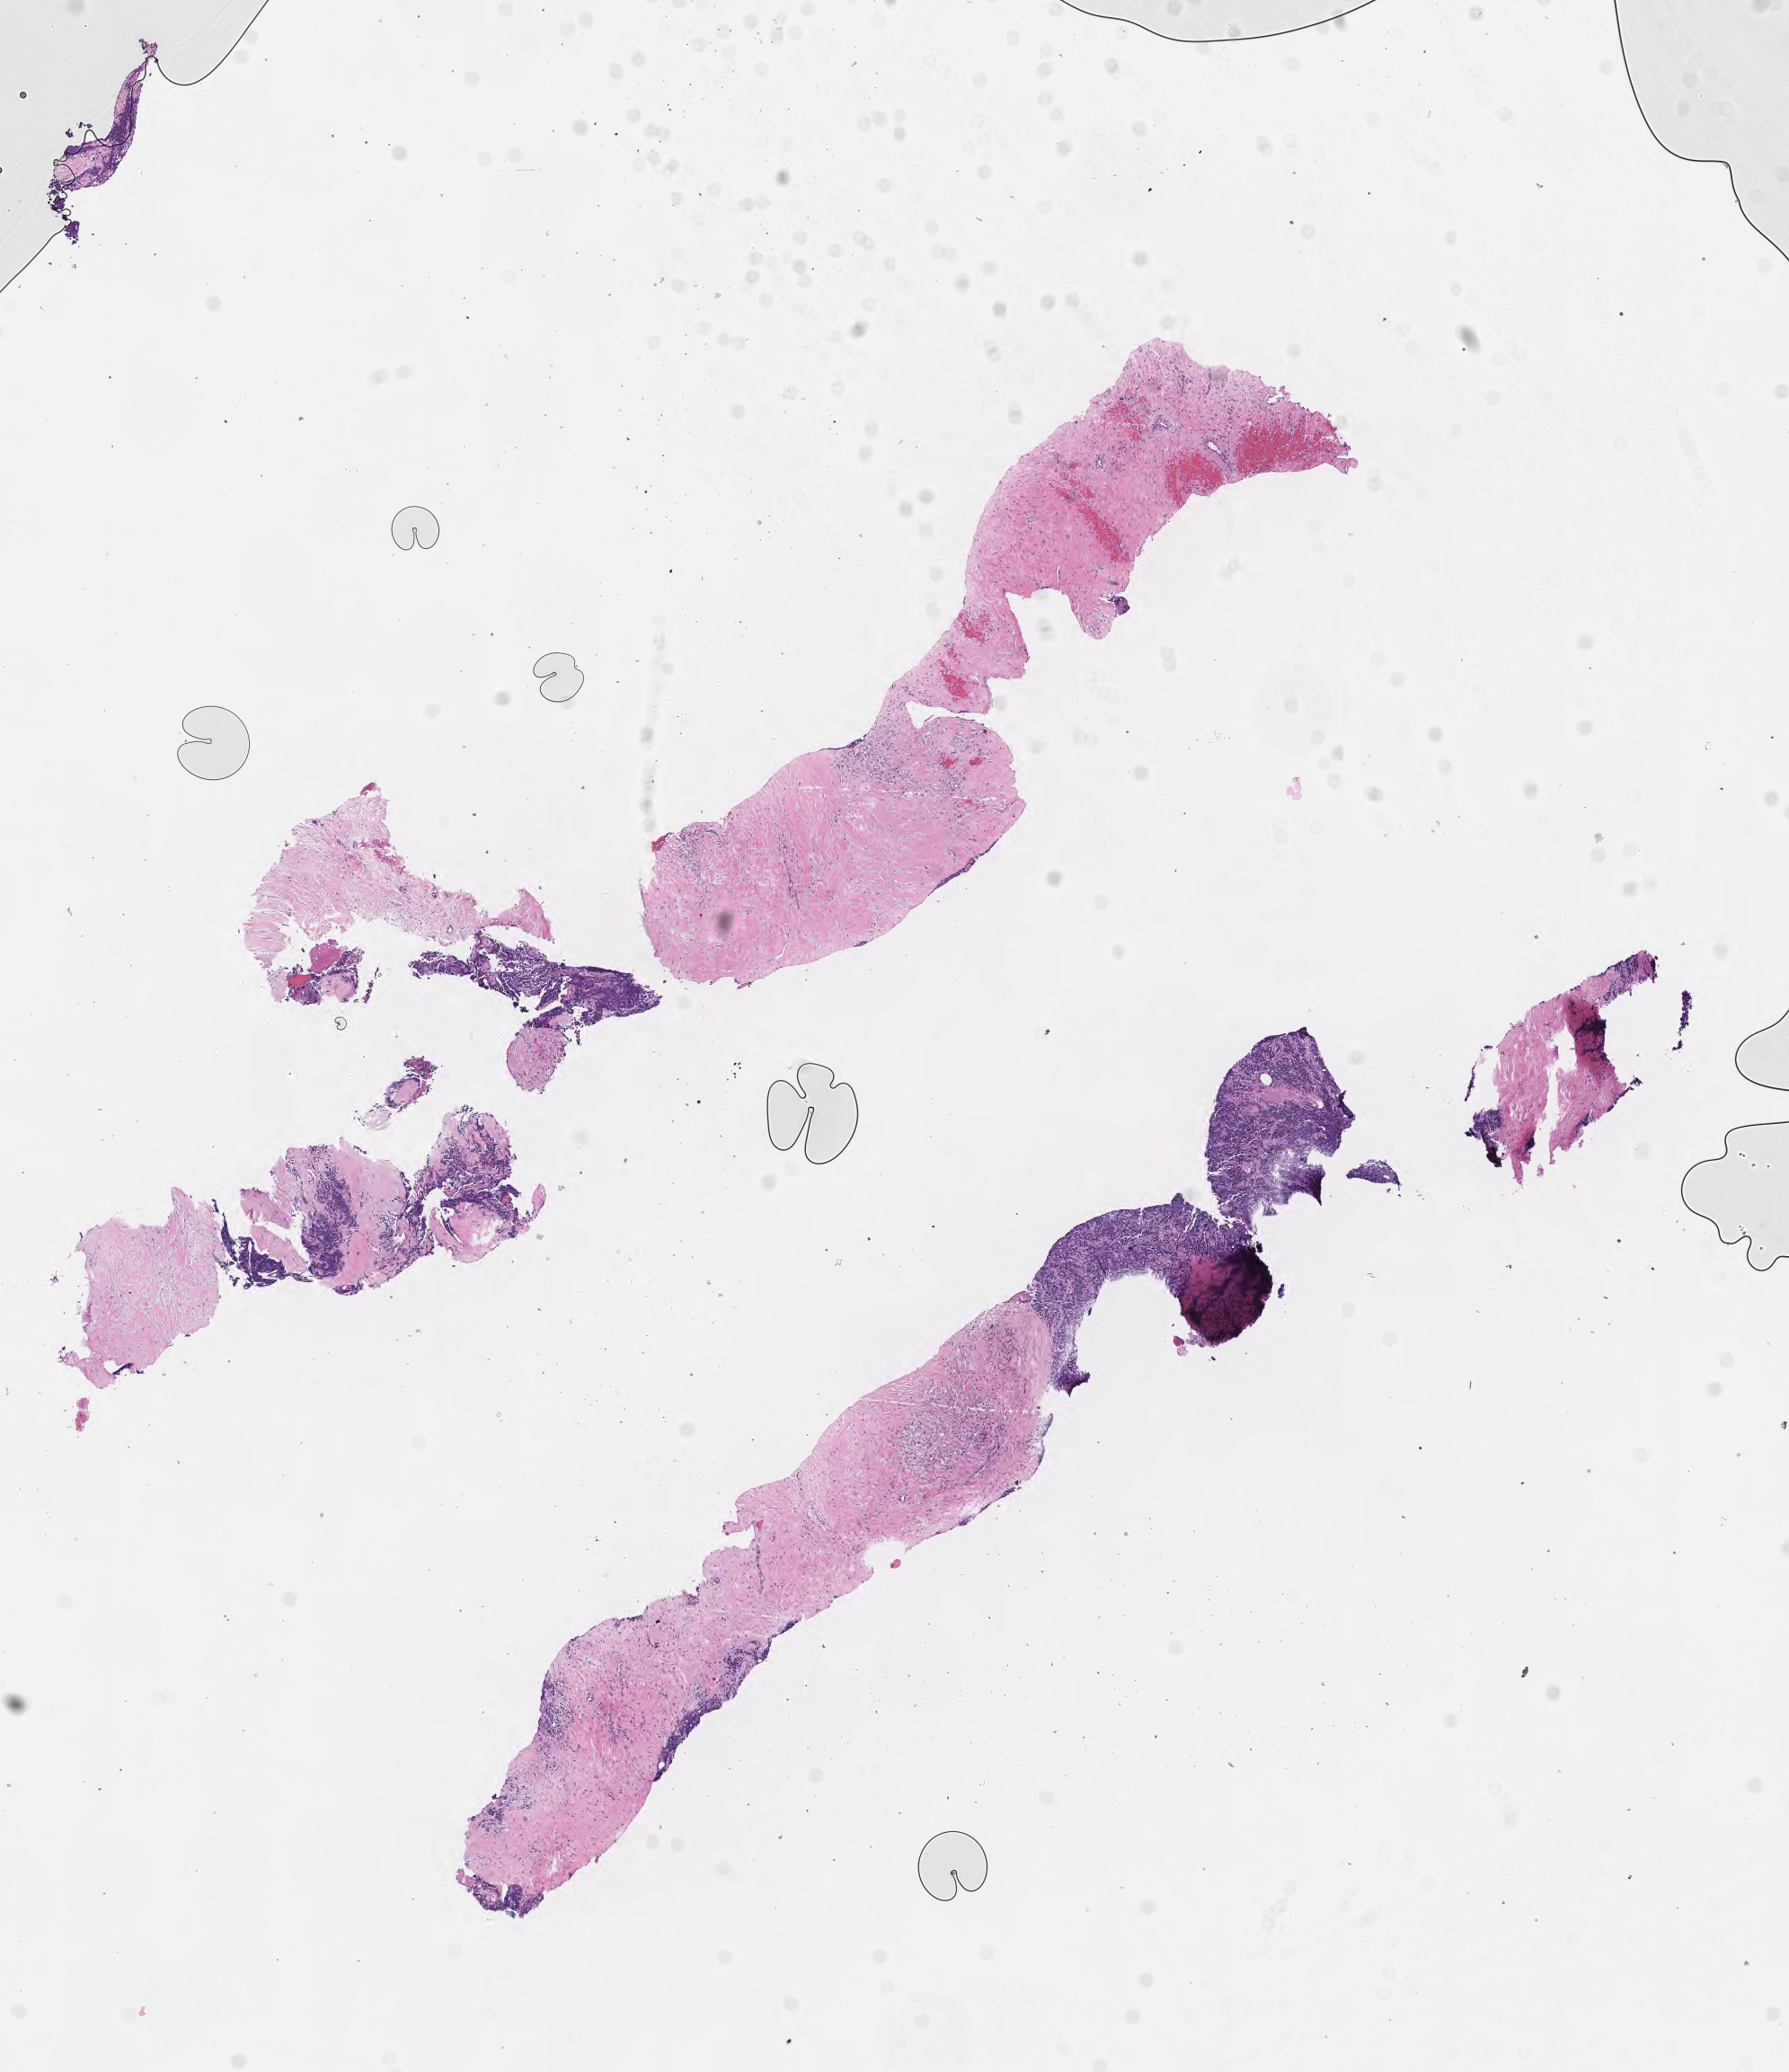
Digitized H&E-stained section of tumor tissue from the soft tissue of trunk, a low-resolution overview of the entire scanned area, about 8.1 x 9.3 mm. Patient female; age 157 months (13 years 1 month).
Specimen: formalin-fixed, paraffin-embedded (FFPE) tissue.